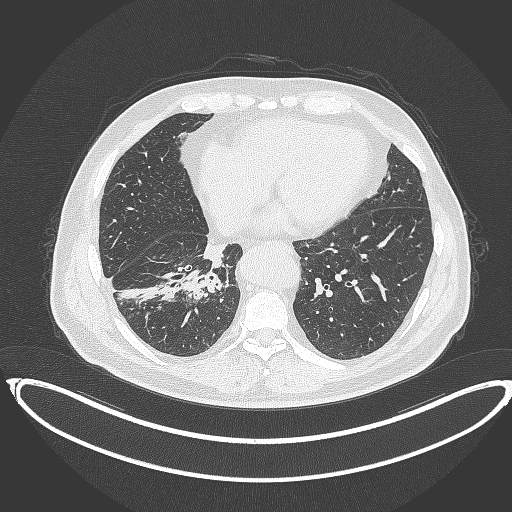
Chest CT, one axial slice. Slice 143 of 387 in the series (ordered by position). Reconstruction kernel B70f. 120 kVp. Lung window (W 1500 / L -600 HU). 1 mm slice thickness. 512 × 512 image matrix. Patient: male, 61 years. From the clinical record (not read from this slice): clinical TNM (as recorded): T1b N1 M0.
Annotated regions visible in this slice (rectangle marked by the reading radiologist):
- lung tumour (recorded histology: squamous cell carcinoma): bounding box <178,264,224,304> (left, top, right, bottom; pixels)